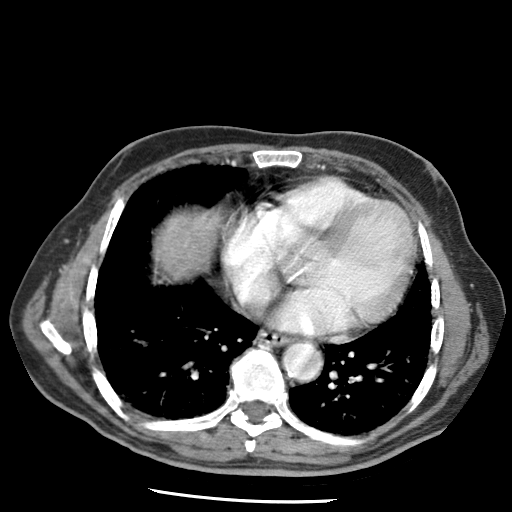
Contrast-enhanced abdominal CT (liver protocol), one axial slice. Slice 68 of 79 in the series (ordered by position). 120 kVp. Soft-tissue window (W 400 / L 40 HU). 2.5 mm slice thickness. 512 × 512 image matrix. Case-level facts recorded for this patient, not image findings: diagnosis: hepatocellular carcinoma (patient treated with transarterial chemoembolisation; whether this scan precedes or follows treatment is not stated here); TNM stage (as recorded): Stage-IIIA; Child-Pugh class: A; tumour differentiation: moderately differentiated; tumour nodularity: multinodular.
Structures marked on this image (semi-automatically segmented with operator editing):
- liver parenchyma outside the tumour (the mass and vessels are separate outlines, so this box may not span the whole liver): bounding box <156,212,220,278> (left, top, right, bottom; pixels)